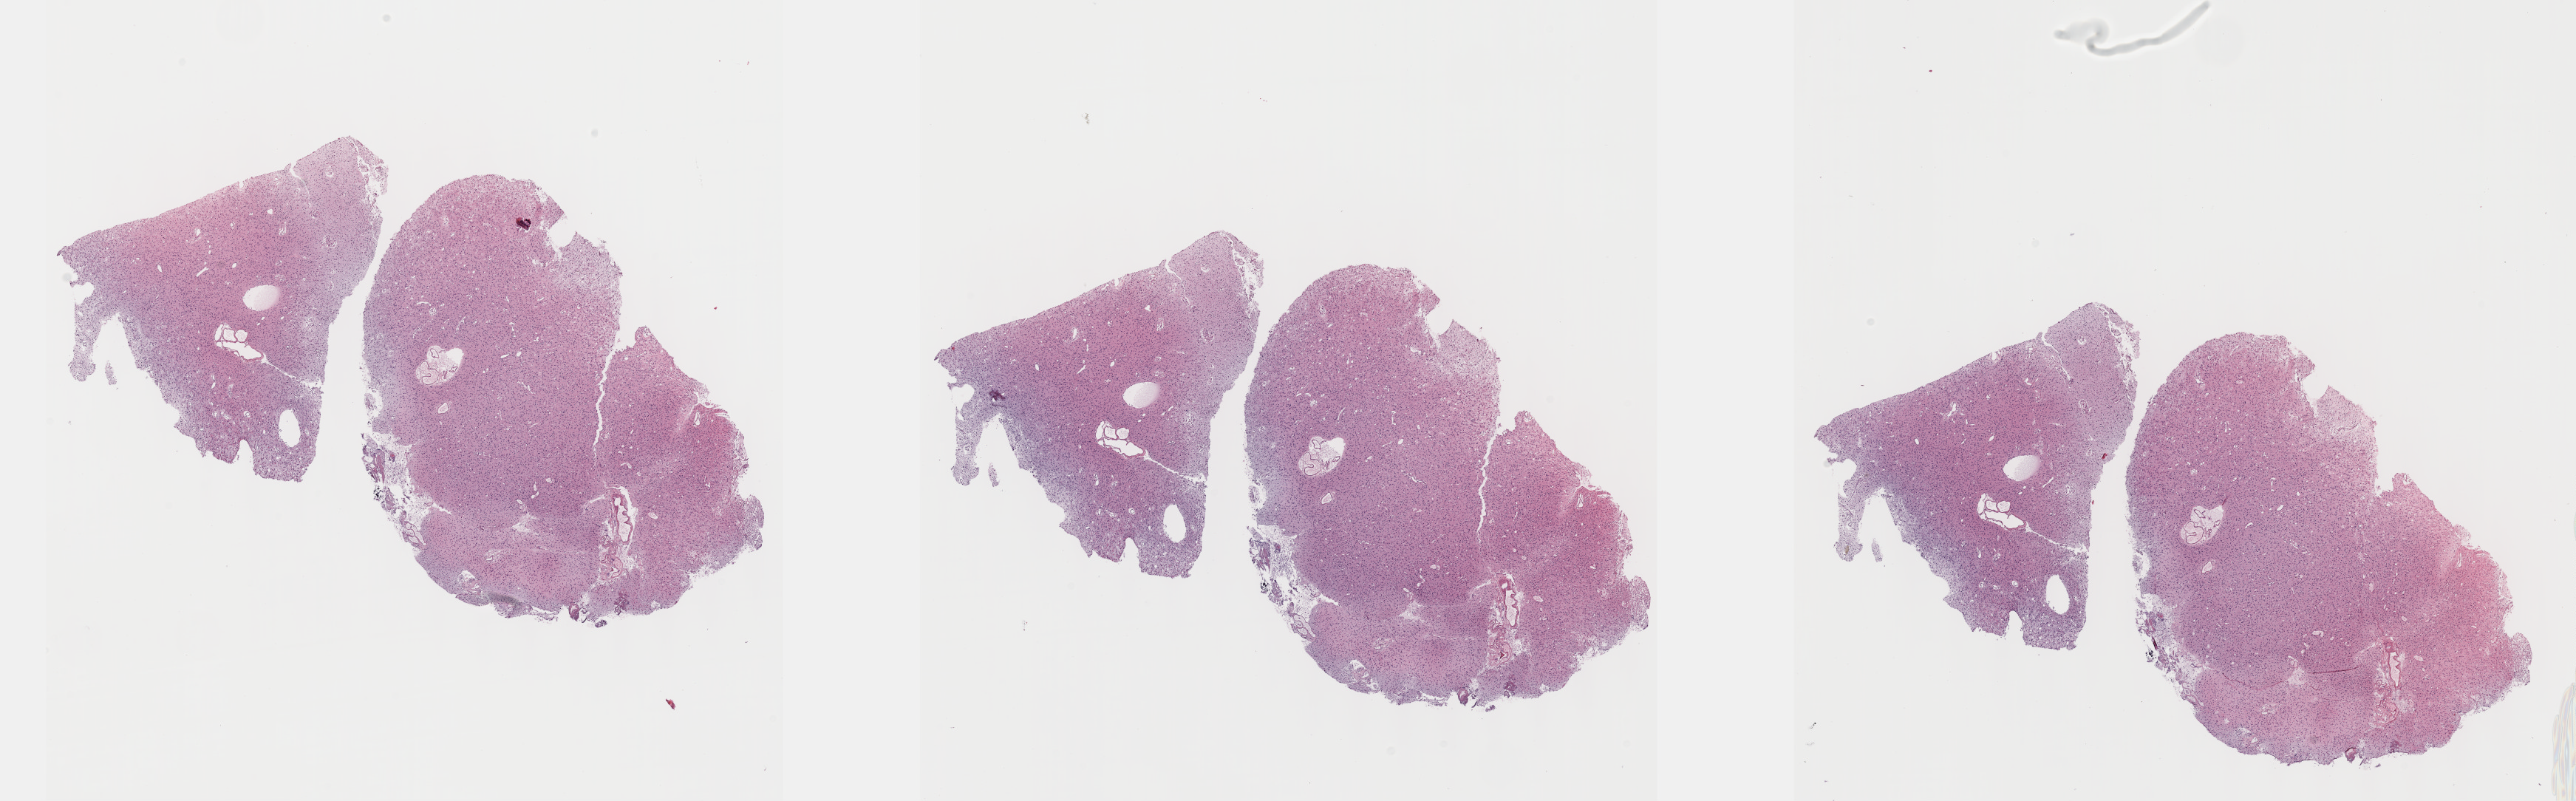
Whole-slide histology image, Hematoxylin and eosin (H&E) stained, whole scanned area (about 28.2 x 8.8 mm) shown as a low-resolution overview; formalin-fixed paraffin-embedded (FFPE) diagnostic section; brain, primary tumour sample. Male patient; age at initial diagnosis 67 years. Histologic grade: G2 (moderately differentiated).
Histologic diagnosis: Mixed glioma.